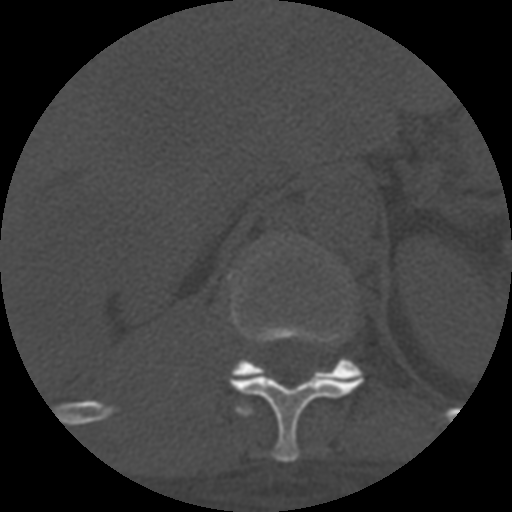
CT including the spine, one axial slice; slice 327 of 708 in the series (ordered by position); reconstruction kernel STANDARD; 120 kVp; one of 3 acquisitions stored at this slice position; bone window (W 1800 / L 400 HU); 1.25 mm slice thickness; 512 × 512 image matrix, field of view 160 × 160 mm. Patient age 55 years. From the clinical record (not read from this slice): primary cancer: colon.
Outlined on this slice (semi-automatically segmented with operator editing):
- T11 vertebra: bounding box <229,243,363,463> (left, top, right, bottom; pixels)
- T12 vertebra: <232,359,363,380>